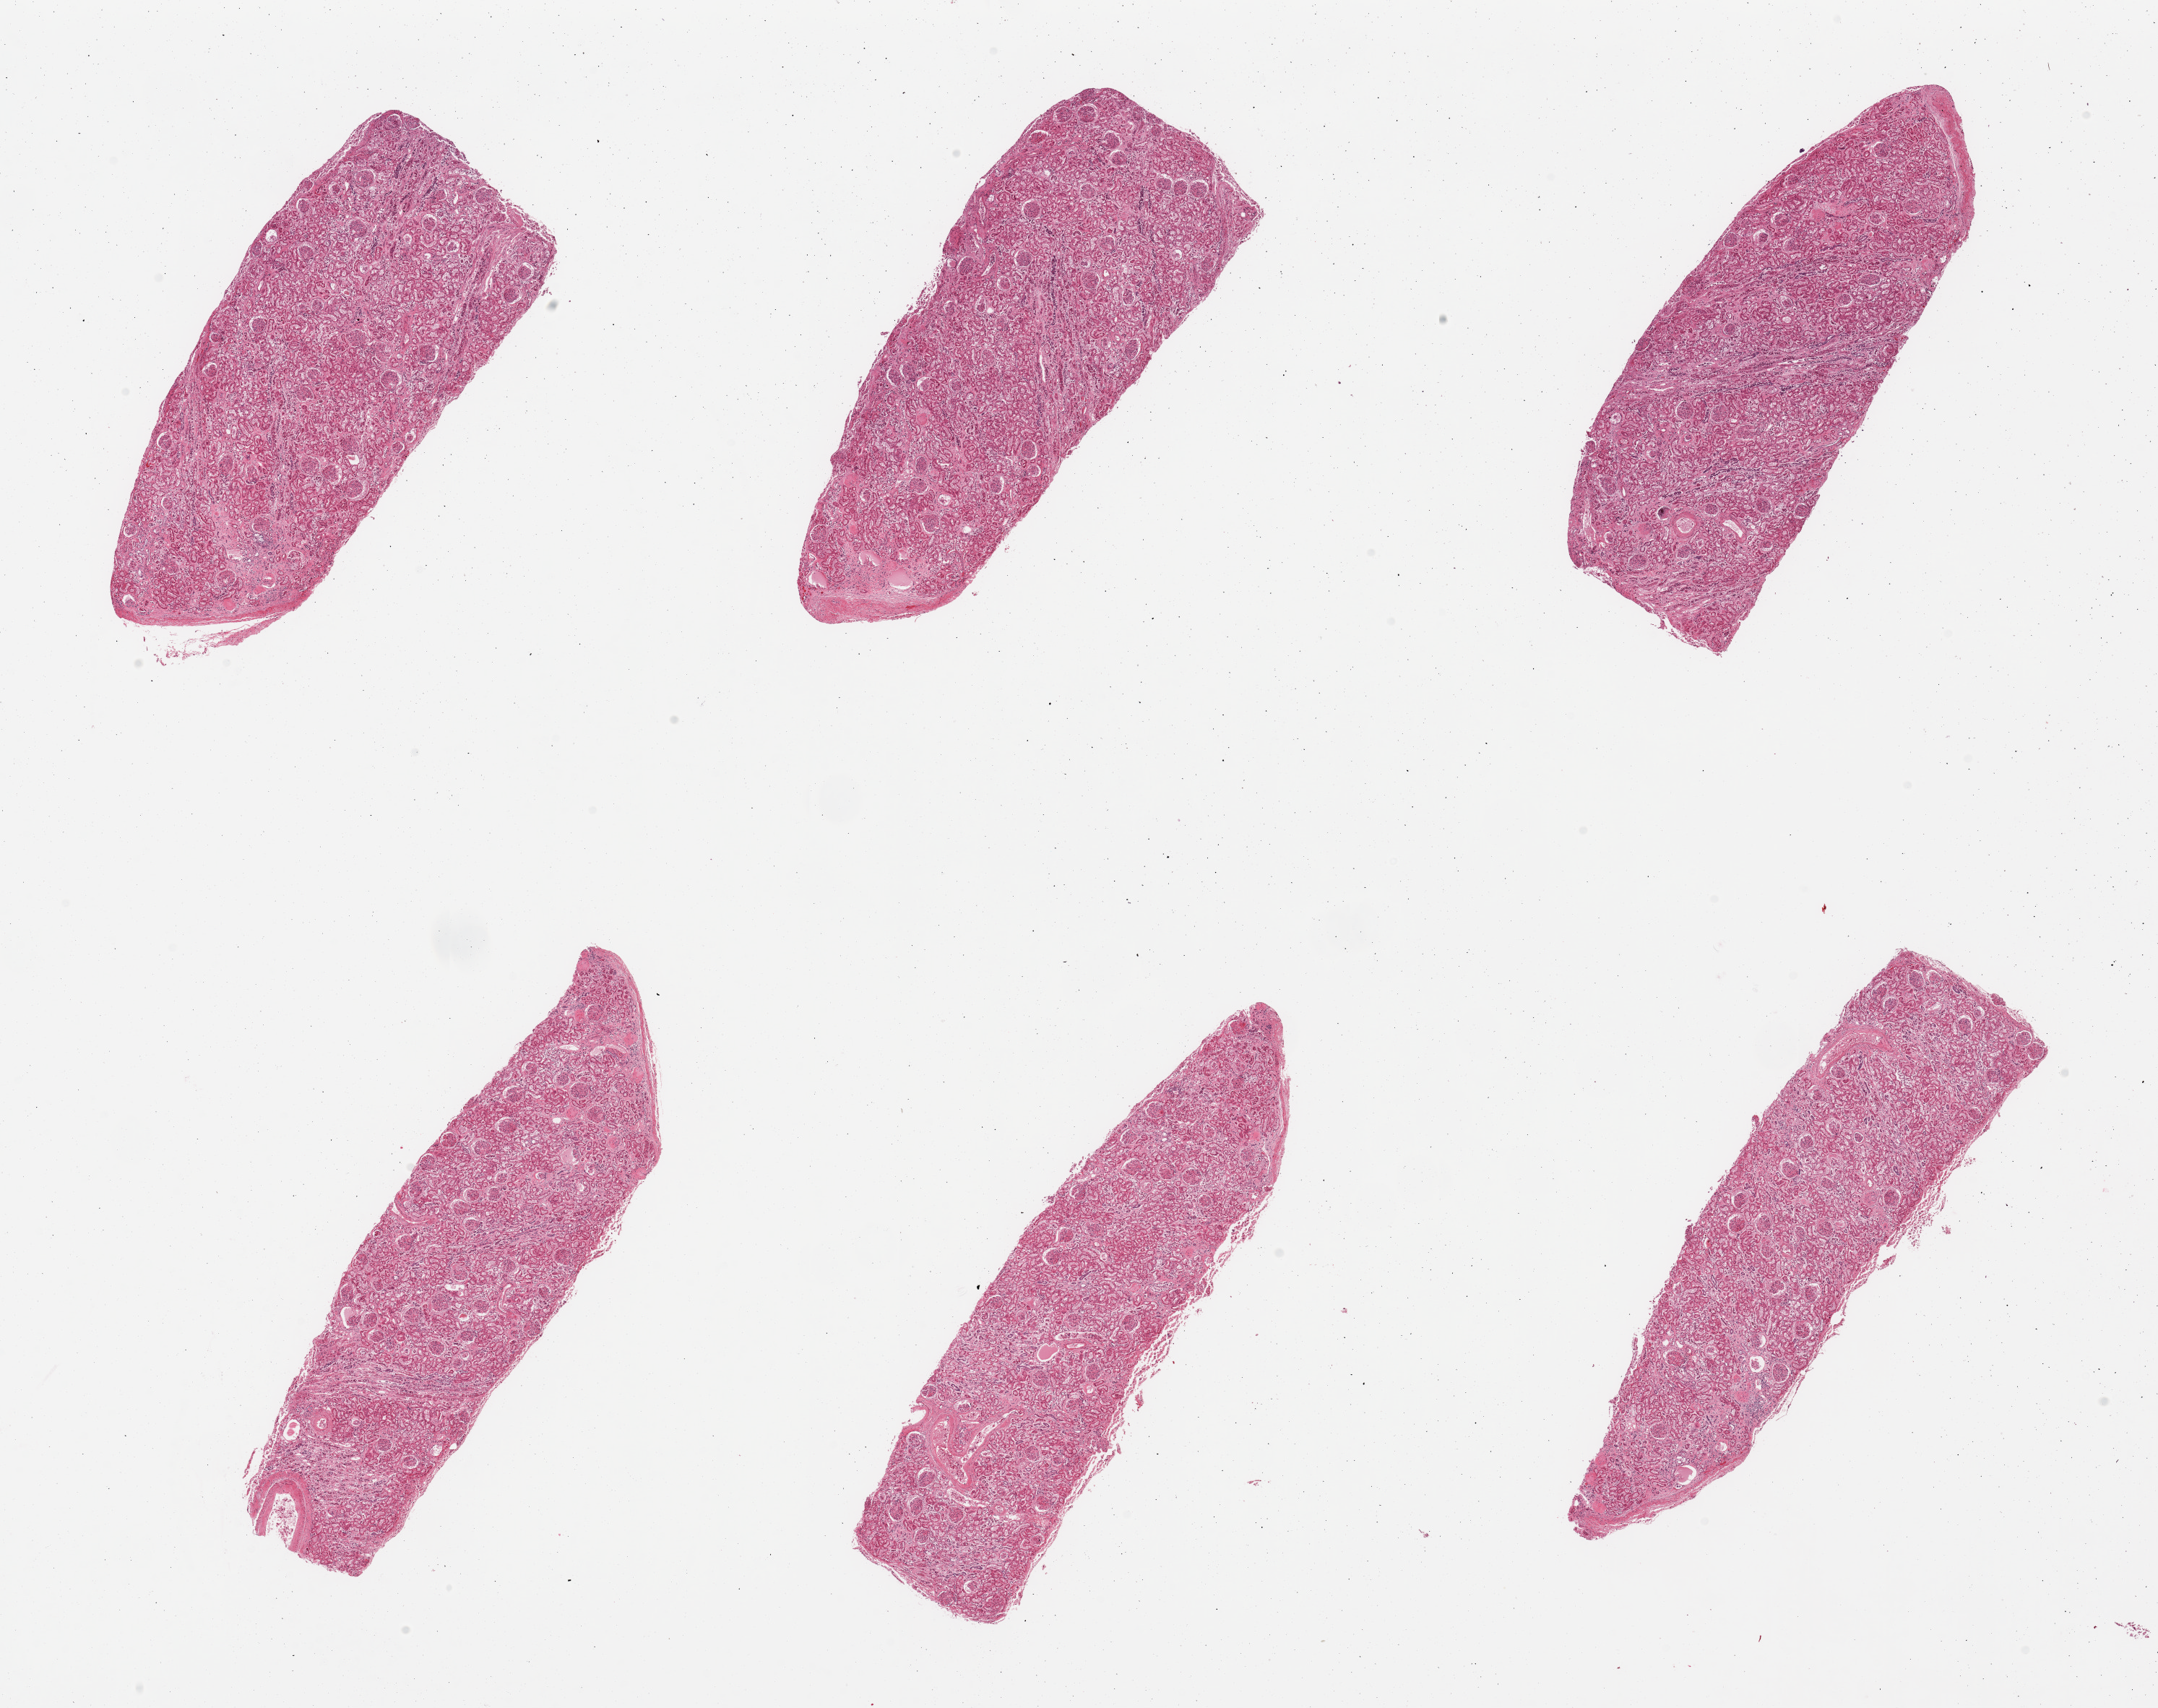
Digitized hematoxylin and eosin (H&E)-stained section — shown as a low-resolution overview of the whole scanned area (about 23.6 x 18.7 mm, acquisition: 20x scan); PAXgene-fixed paraffin-embedded (PFPE) section; section of renal cortex (target tissue); donor tissue sample. Female donor.
Review note (as recorded): 6 pieces.